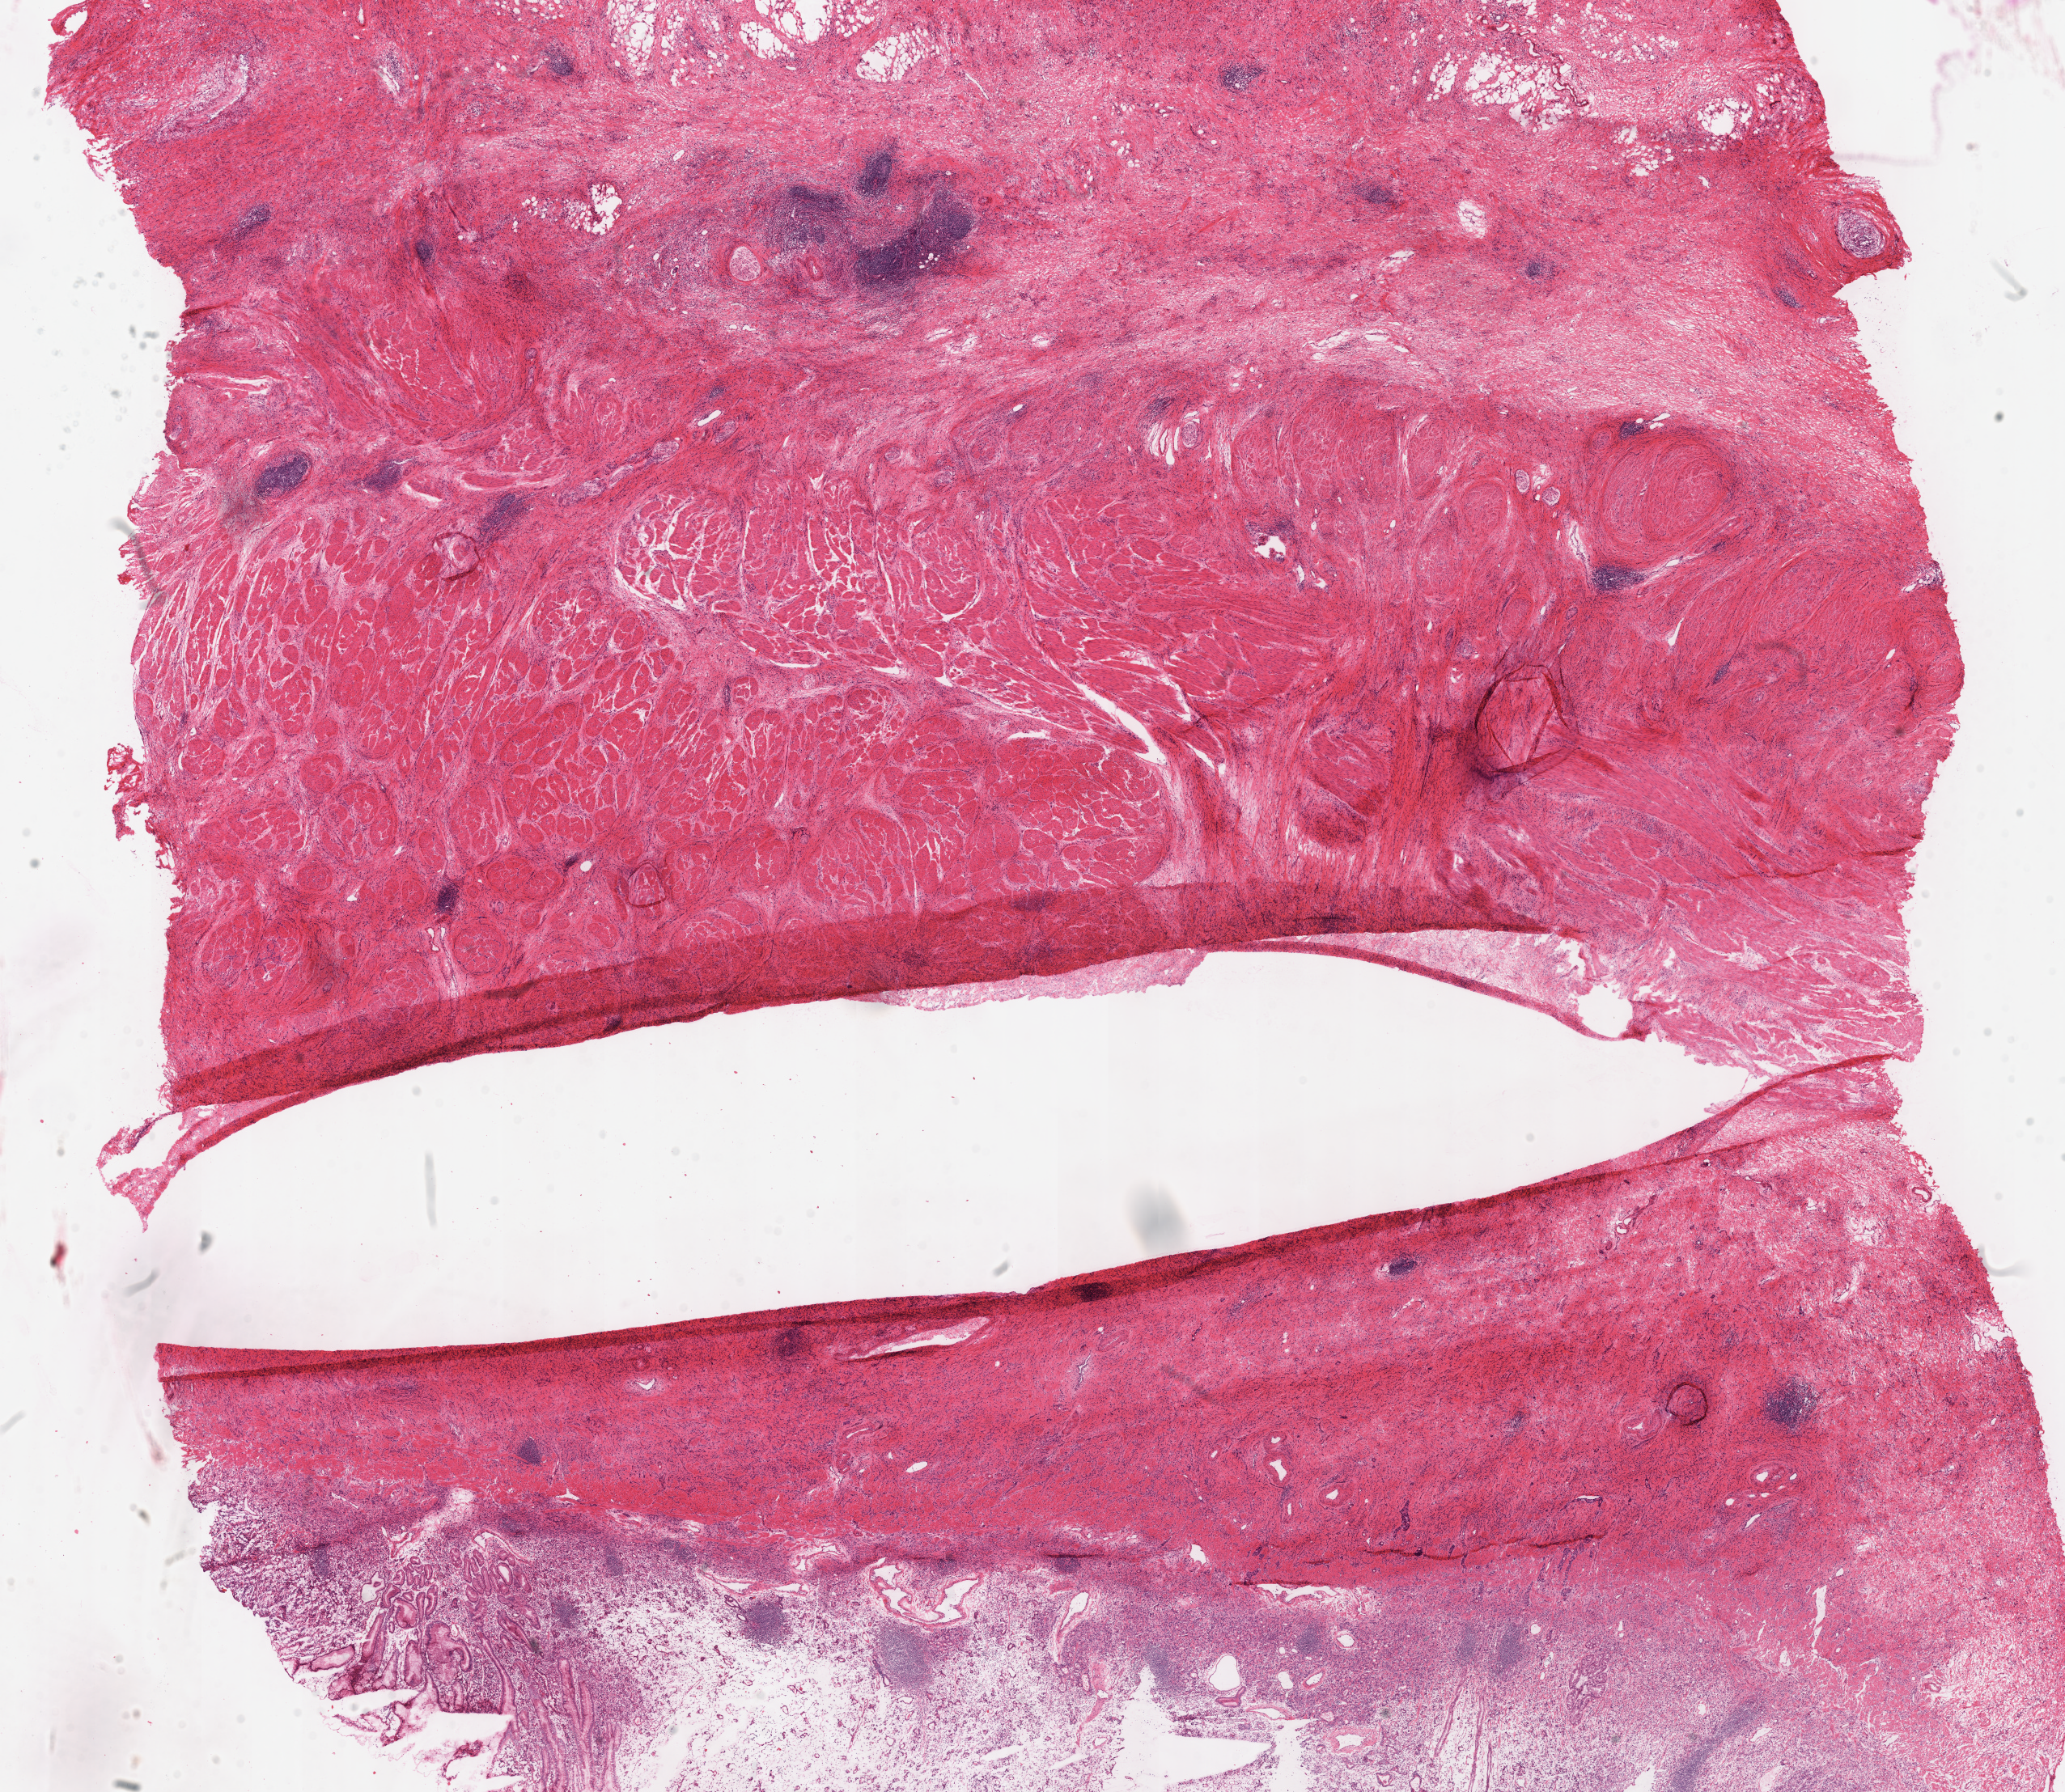
Digitized H&E tissue section (whole slide) — low-resolution overview of the scanned area, about 20.1 x 17.4 mm; frozen section; sample: primary tumour, stomach. Patient: male, age at initial diagnosis 62 years. Histologic grade: G3 (poorly differentiated). Slide review estimates, as recorded: tumour cells 65%, tumour nuclei 65%, normal cells 10%, stromal cells 25%, necrosis 0%.
TNM: T3 N3a M0. Lymph nodes positive (case pathology): 10 of 15 examined. Diagnosis: Adenocarcinoma, NOS (cardia, NOS). AJCC pathologic stage: IIIB (7th edition).